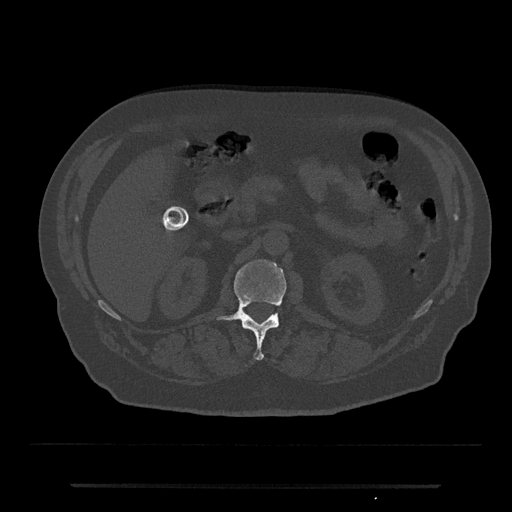
CT including the spine, one axial slice. Slice 529 of 797 in the series (ordered by position). 120 kVp. Bone window (W 1800 / L 400 HU). 0.5 mm slice thickness. 512 × 512 image matrix. Male patient, age 80 years. From the clinical record (not read from this slice): primary cancer: prostate; vertebrae with lytic lesions (as recorded): L1, T11.
Structures marked on this image (semi-automatic segmentation, software-assisted and operator-edited):
- L1 vertebra: bounding box [x1, y1, x2, y2] px = [216, 259, 287, 360]